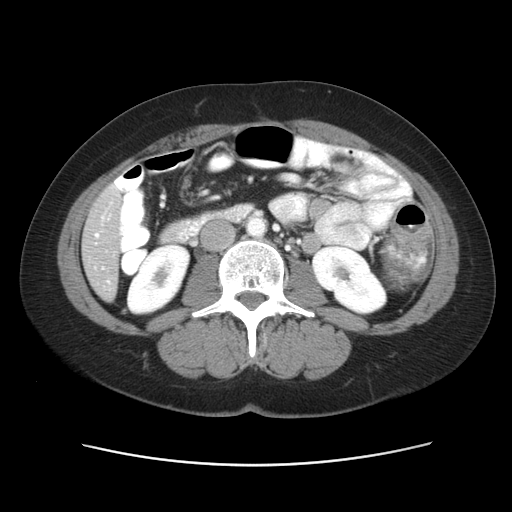
Contrast-enhanced abdominal CT, one axial slice; slice 16 of 52 in the series (ordered by position); 120 kVp; intravenous contrast given; soft-tissue window (W 400 / L 40 HU); 5 mm slice thickness; 512 × 512 image matrix. Female patient, age 48 years. Case-level facts recorded for this patient, not image findings: diagnosis: colorectal cancer liver metastases, imaged before liver resection; multiple liver metastases: yes; largest metastasis: 4.5 cm.
Annotated regions visible in this slice (outlined manually by an expert reader):
- hepatic veins: bounding box (x1, y1, x2, y2) in pixels: (95, 216, 110, 283)
- liver: (83, 189, 120, 298)